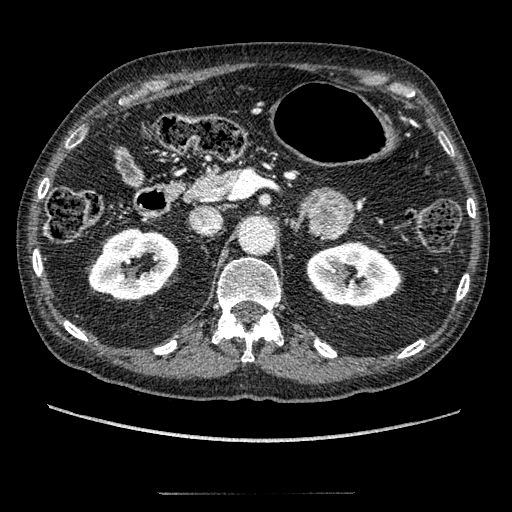
Contrast-enhanced abdominal CT, one axial slice; position 122 of 274 along the scan axis; reconstruction kernel STANDARD; 120 kVp; soft-tissue window (W 400 / L 40 HU); 512 × 512 image matrix, field of view 381 × 381 mm. Patient: male, 69 years. Case-level facts recorded for this patient, not image findings: diagnosis: adrenocortical carcinoma; tumour side: left adrenal; tumour size at pathology: 6.1 cm; Ki-67 index: 10 %; stage (as recorded): 3.
Outlined on this slice (semi-automatic segmentation, software-assisted and operator-edited):
- mass: bounding box <302,188,352,239> (left, top, right, bottom; pixels)